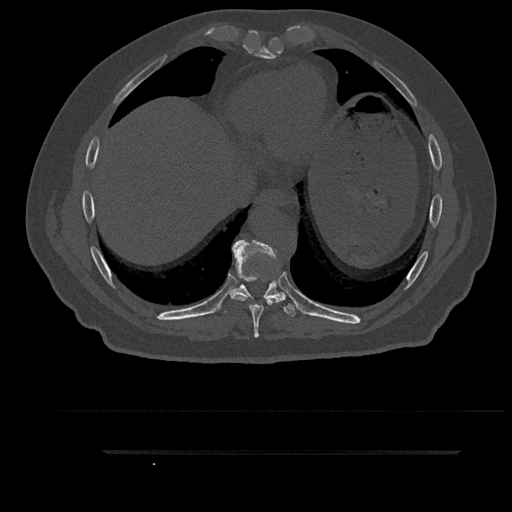
CT including the spine, one axial slice; slice 449 of 797 in the series (ordered by position); reconstruction kernel Br40s/3; 120 kVp; bone window (W 1800 / L 400 HU); 512 × 512 image matrix. Patient: male, 63 years. Case-level facts recorded for this patient, not image findings: primary cancer: renal; vertebrae with lytic lesions (as recorded): T8.
Annotated regions visible in this slice (semi-automatic segmentation, software-assisted and operator-edited):
- T10 vertebra: bounding box <283,295,286,297> (left, top, right, bottom; pixels)
- T8 vertebra: <231,239,286,338>
- T9 vertebra: <216,251,296,317>